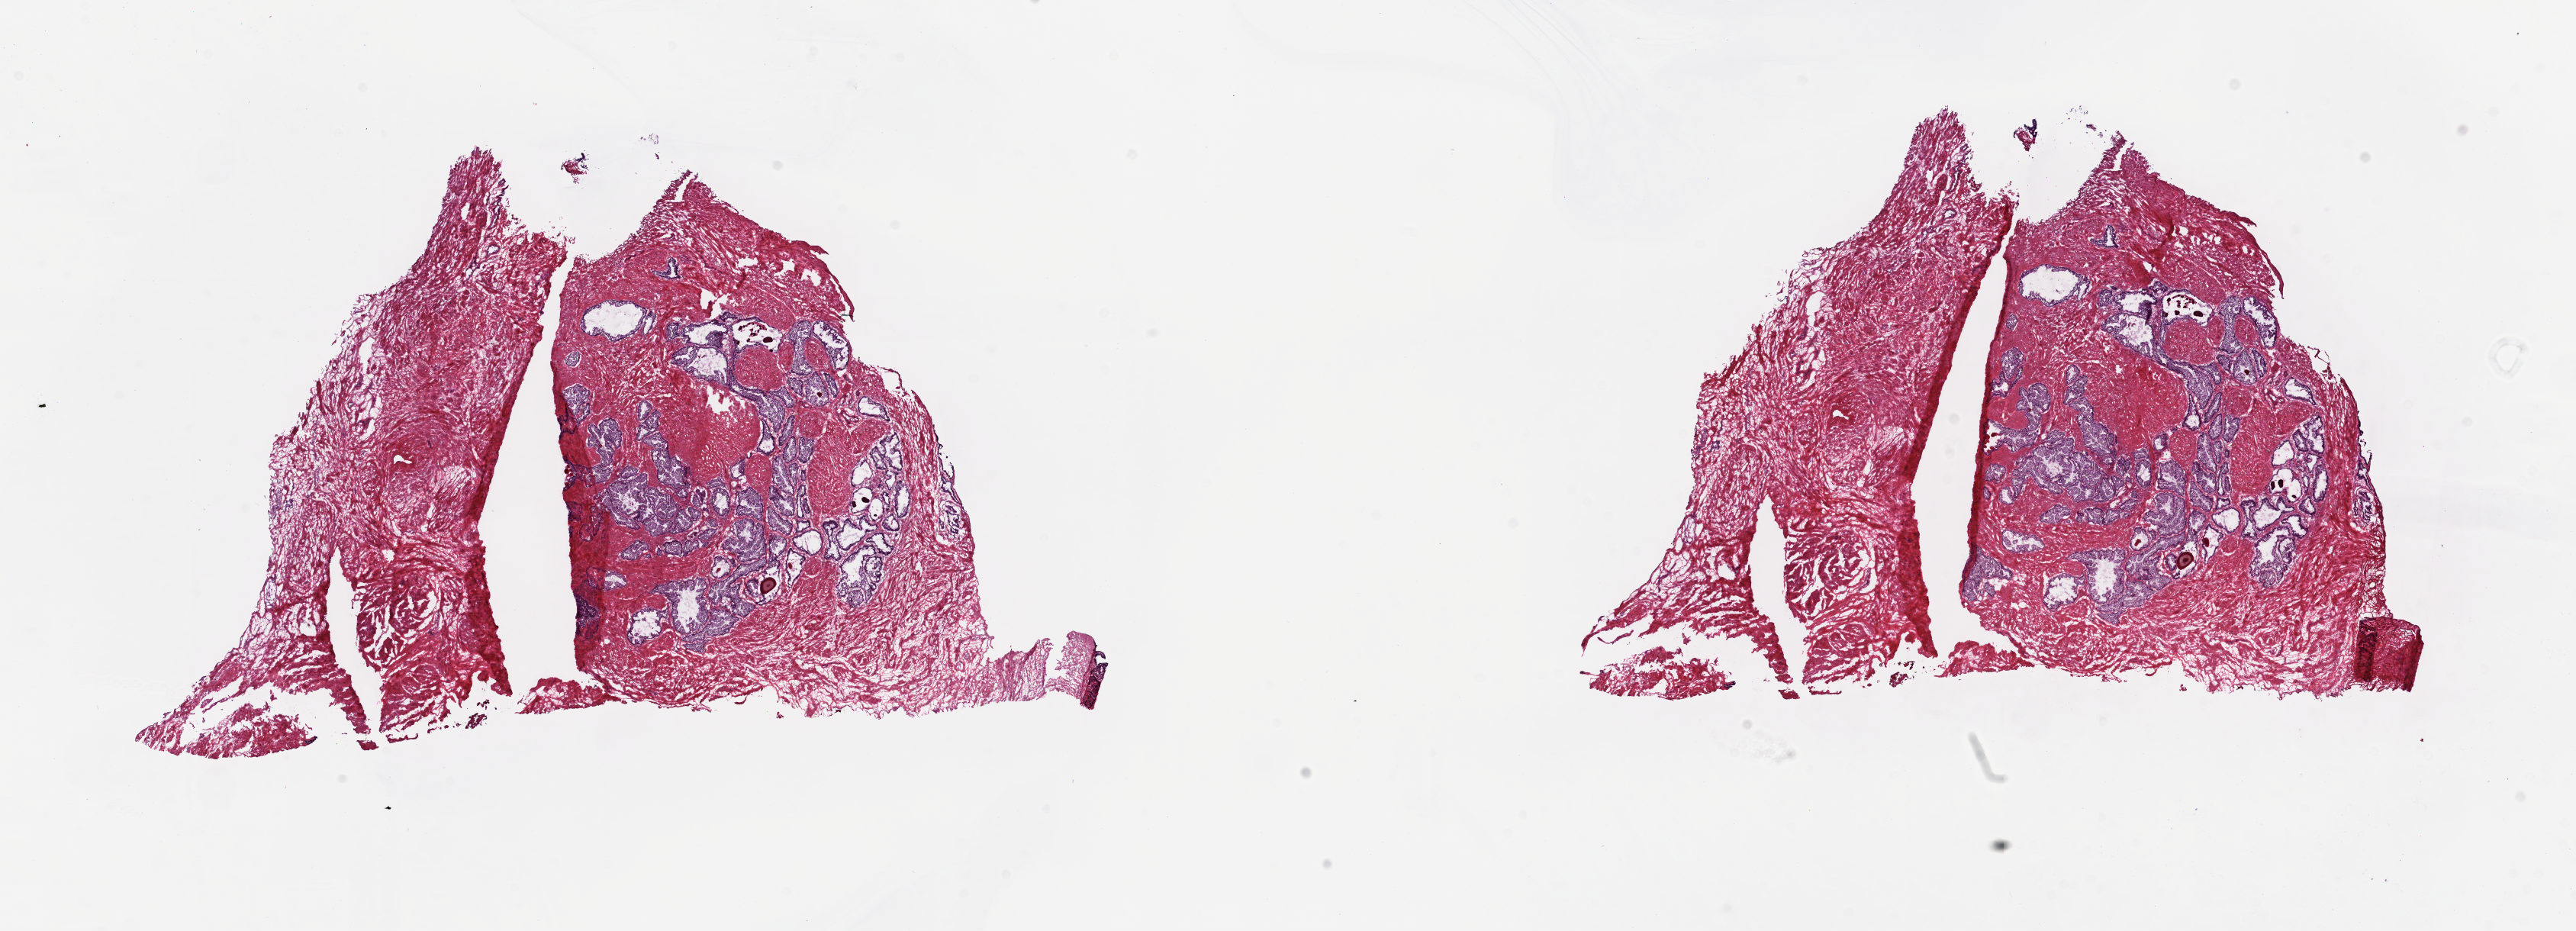
H&E-stained whole-slide image, whole scanned area (about 26.8 x 9.7 mm) shown as a low-resolution overview, frozen section from the top of the tissue portion, solid tissue normal (non-tumour tissue) sample from the prostate. Male, age 51 years at initial diagnosis. Pathologist review of this section (percent, as recorded): tumour cells 0%, tumour nuclei 0%, normal cells 25%, stromal cells 75%, necrosis 0%. Infiltration values recorded for this section: lymphocyte infiltration 0%, monocyte infiltration 0%, neutrophil infiltration 0%.
- this section: solid tissue normal (non-tumour) sample from the same patient
- patient diagnosis: Infiltrating duct carcinoma, NOS (prostate gland)